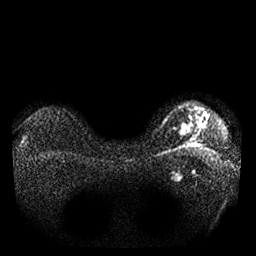
Breast MRI, one axial slice. Position 22 of 25 along the scan axis. Diffusion-weighted series; image 2 of 4 stored at this slice position (different b-values; order by instance number). 1.5 T. 4 mm slice thickness. 256 × 256 image matrix, field of view 340 × 340 mm. Female patient.
Outlined on this slice (expert manual segmentation):
- tumour on diffusion-weighted imaging: bounding box <178,127,194,137> (left, top, right, bottom; pixels)